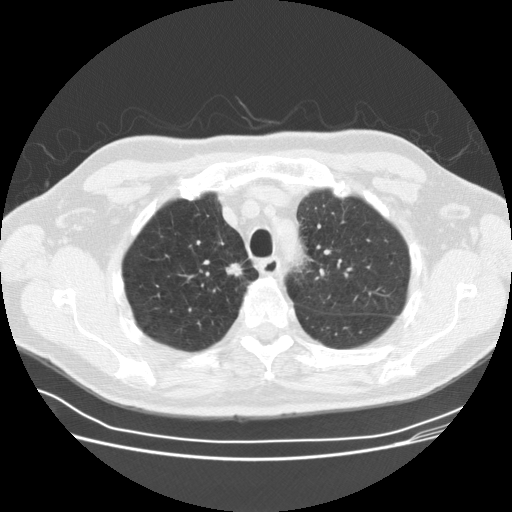
Axial slice from a low-dose chest CT screening exam; third annual screen; lung window (W 1500 / L -600 HU); 2.5 mm slice thickness; standard (soft-tissue) reconstruction kernel (STANDARD); 120 kVp; slice 126 of 164 in the series. Male, age 69 years at enrolment.
Expert reader's lesion annotation, bounding box <220,256,256,290> (left, top, right, bottom; pixels). Reader record for this screening exam (exam-level; its link to the box is not recorded): non-calcified nodule or mass ≥4 mm, right upper lobe, 12 × 10 mm, spiculated (stellate) margins, soft tissue attenuation, pre-existing on the prior screen: yes; interval growth: yes. Official screen result: positive, other.